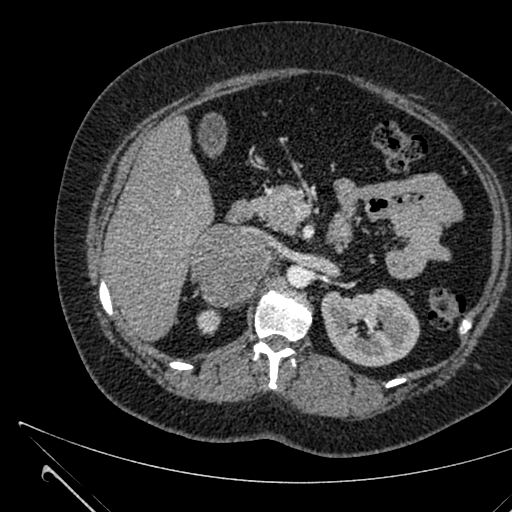
Contrast-enhanced abdominal CT, one axial slice; slice 390 of 731 in the series (ordered by position); intravenous contrast given; soft-tissue window (W 400 / L 40 HU); 1 mm slice thickness; 512 × 512 image matrix, field of view 376 × 376 mm. Patient: female, 36 years. From the clinical record (not read from this slice): diagnosis: adrenocortical carcinoma; tumour side: right adrenal; tumour size at pathology: 10 cm; Ki-67 index: 20 %; stage (as recorded): 4.
Structures marked on this image (semi-automatic segmentation, software-assisted and operator-edited):
- mass: bounding box [x1, y1, x2, y2] px = [191, 225, 266, 305]